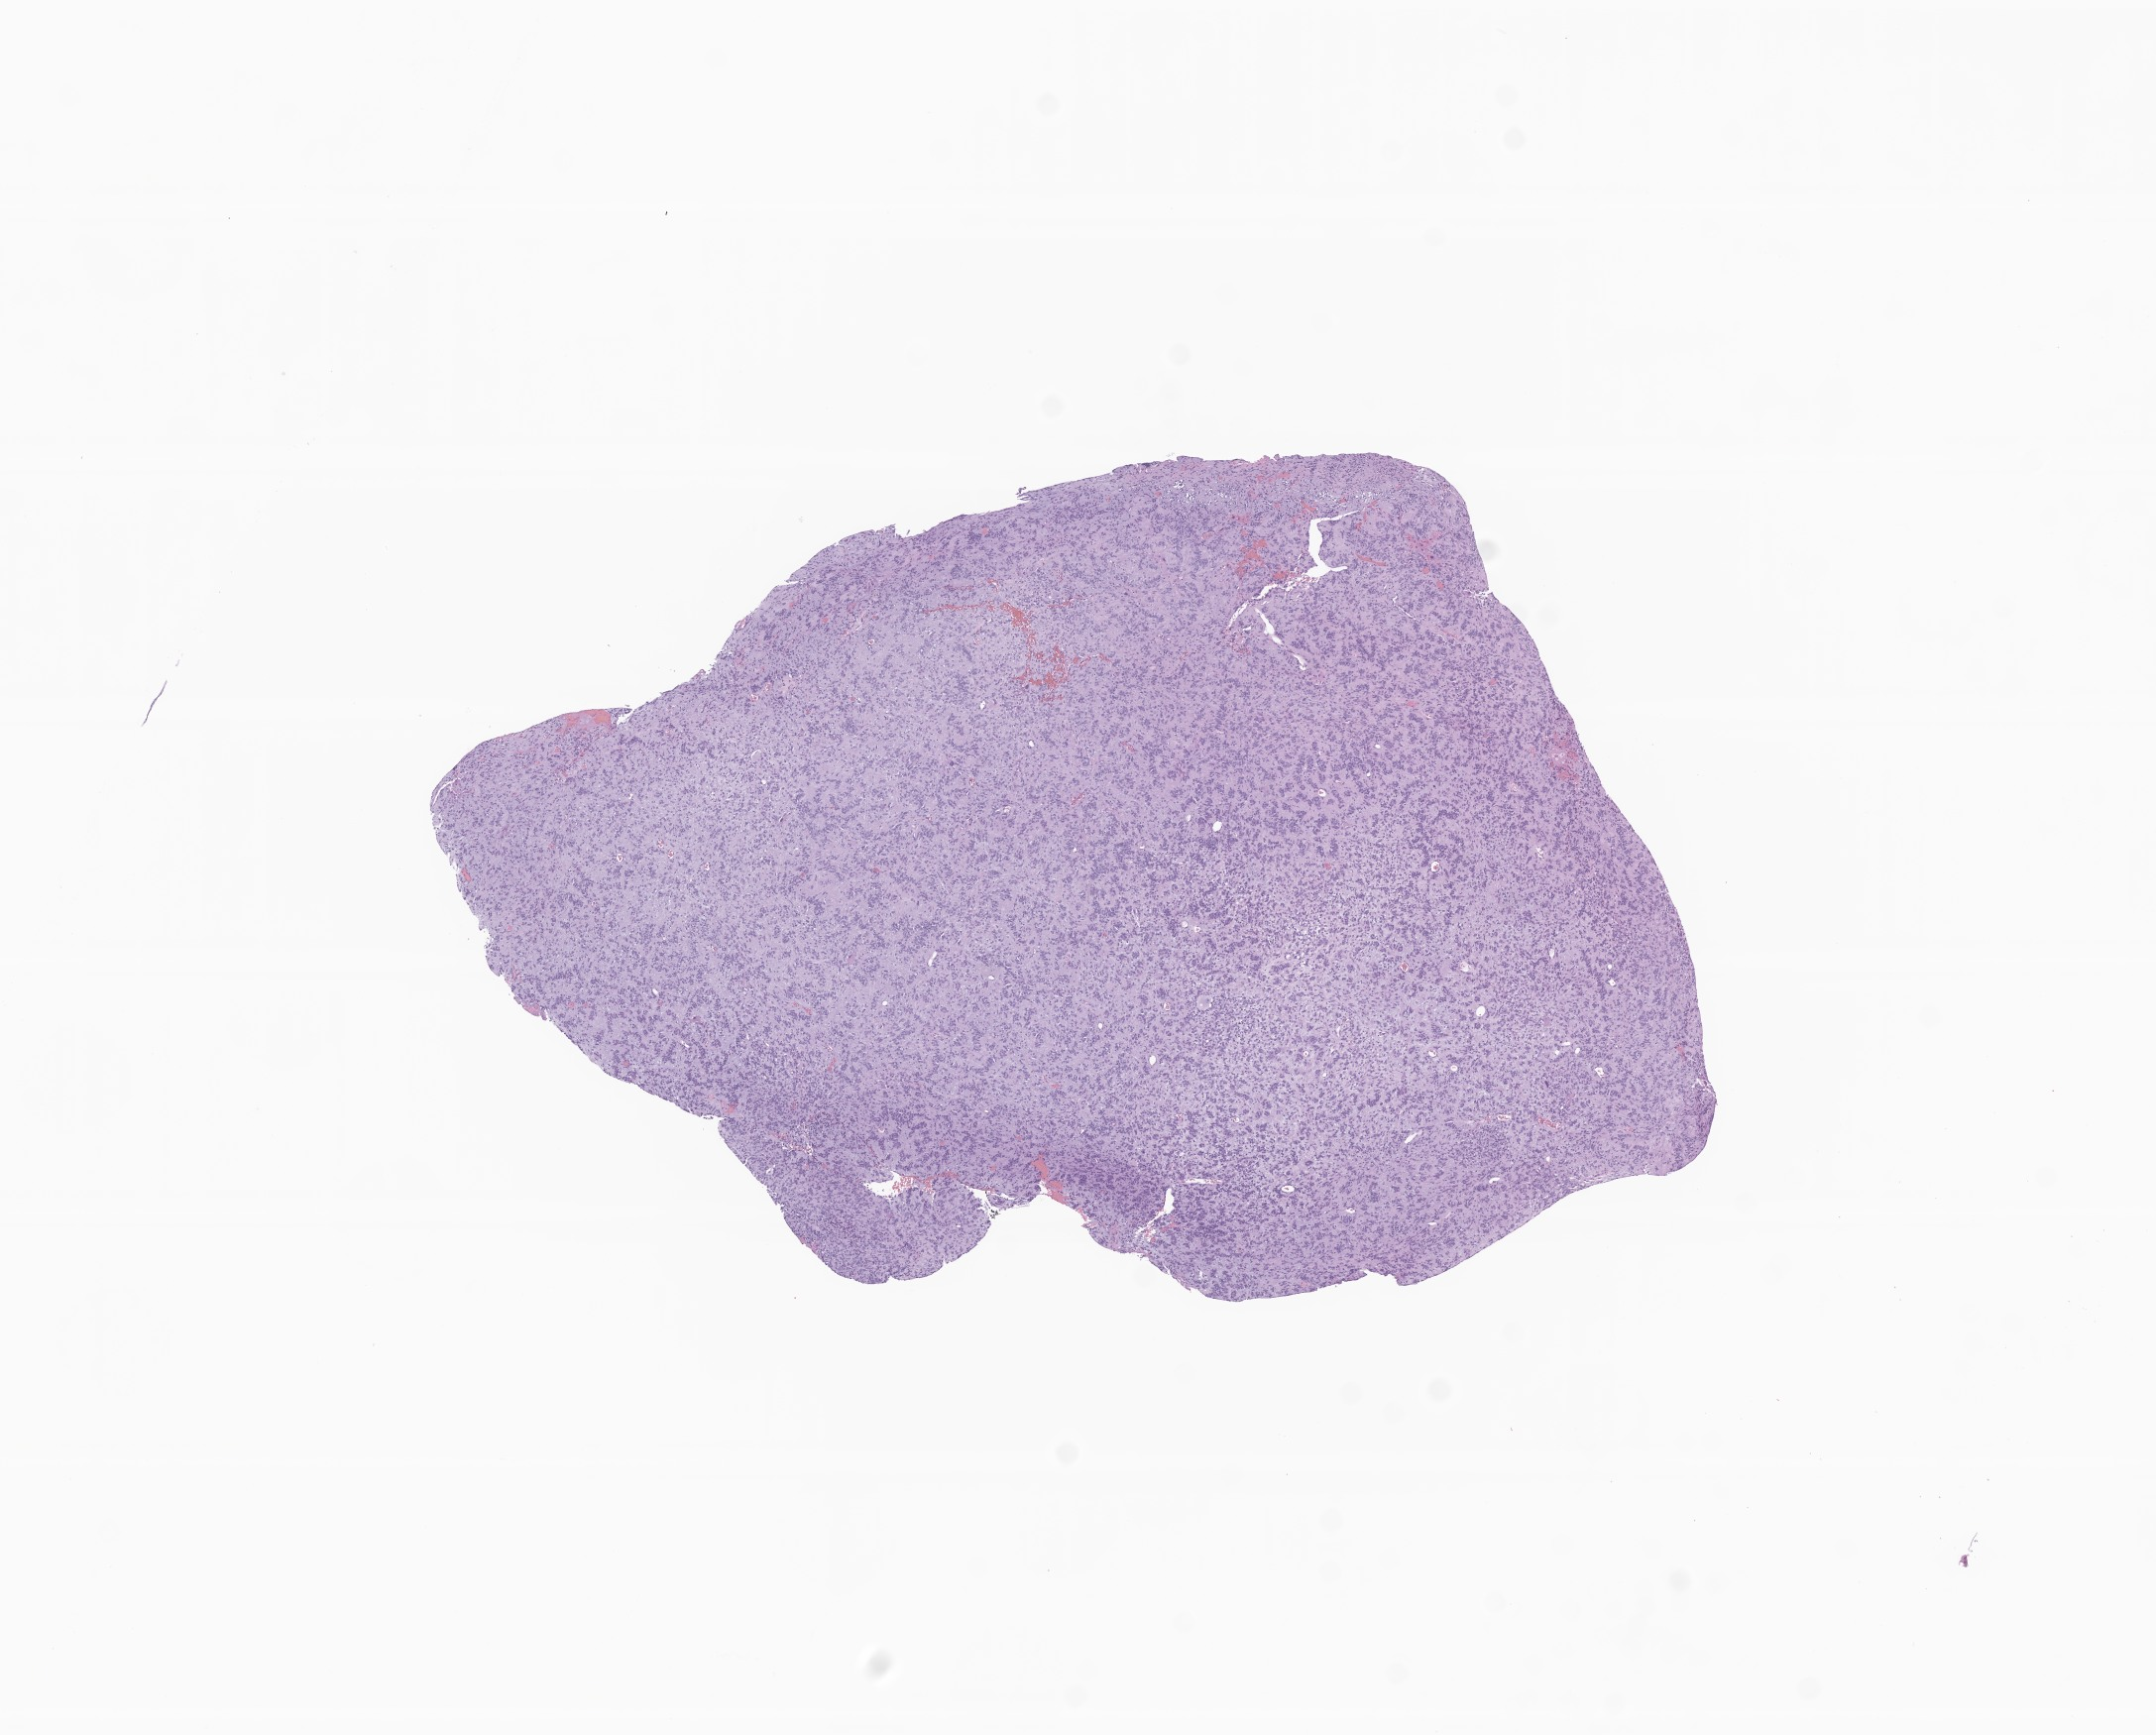
Whole-slide image, hematoxylin and eosin (H&E) stain of tumor tissue from the brain — low-resolution overview of the scanned area, about 9.2 x 7.4 mm. FFPE section. Patient: male, age 123 months.
- recorded diagnosis: Ependymoma, NOS